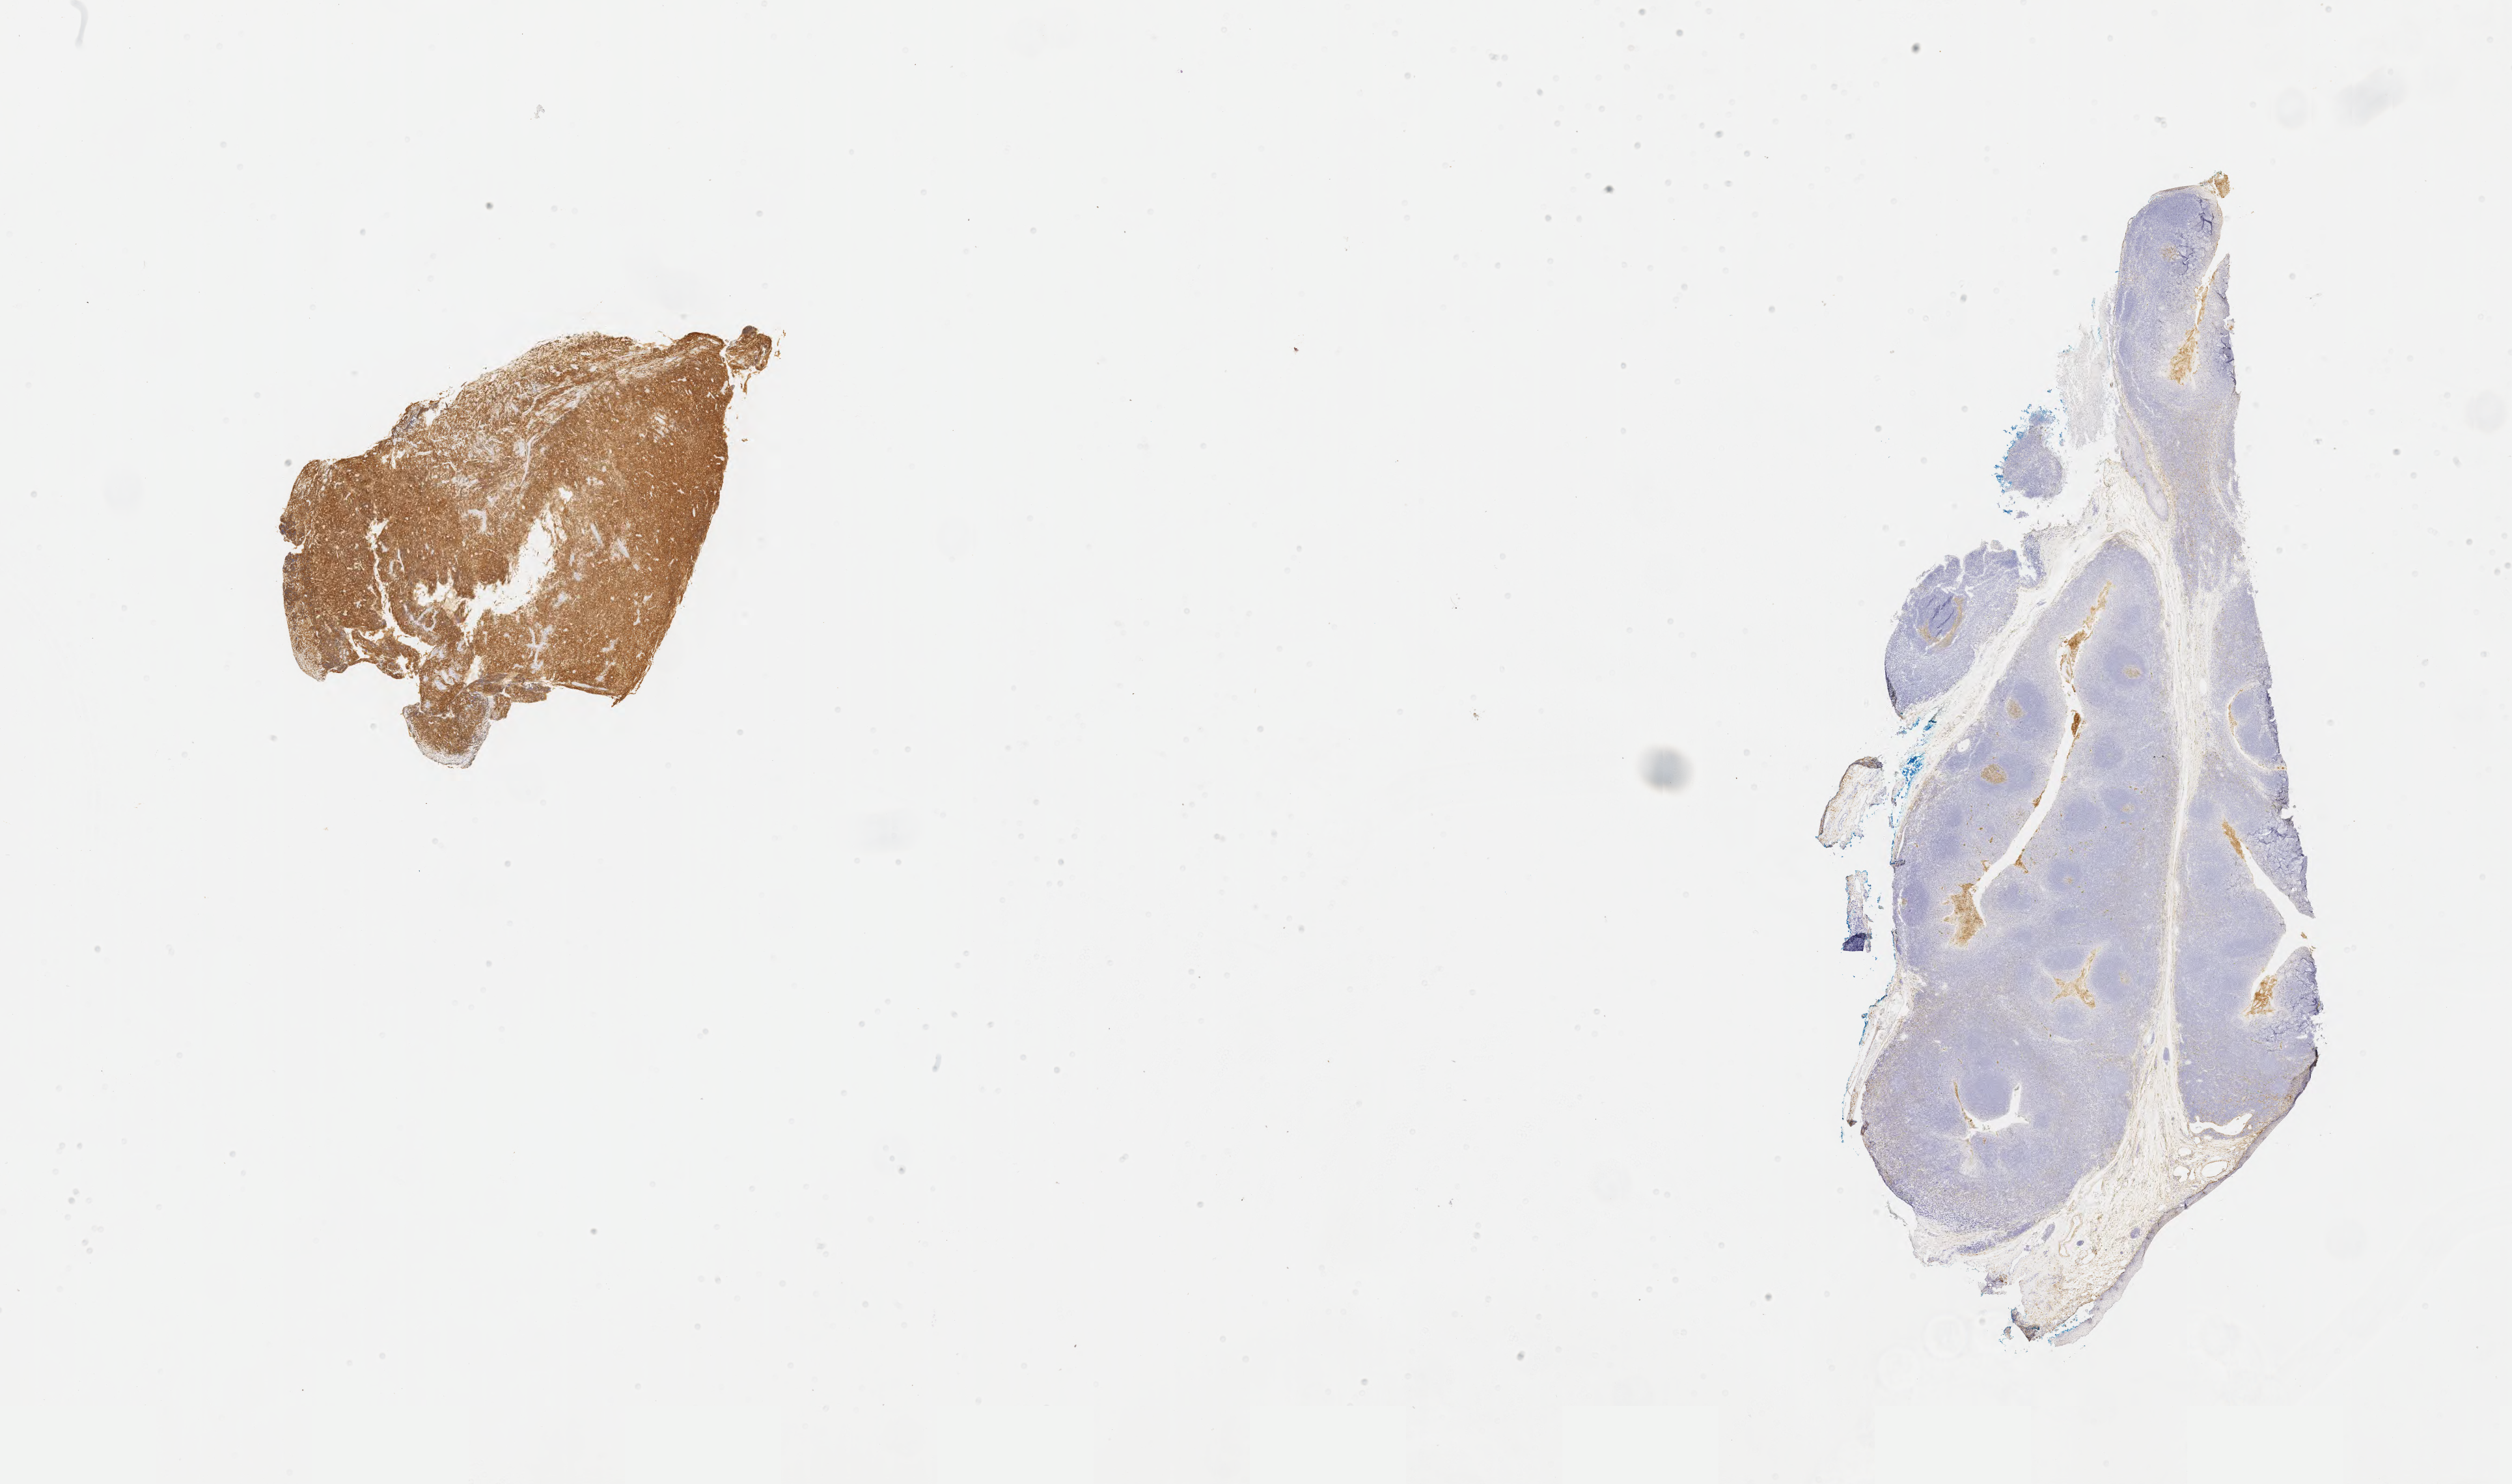
IHC for CD10, whole-slide image — low-resolution overview of the scanned area, about 31.2 x 18.4 mm. Specimen: tumor tissue. Site: ovary. Female patient; age at initial diagnosis 3 years.
Diagnosis: Burkitt lymphoma, NOS.